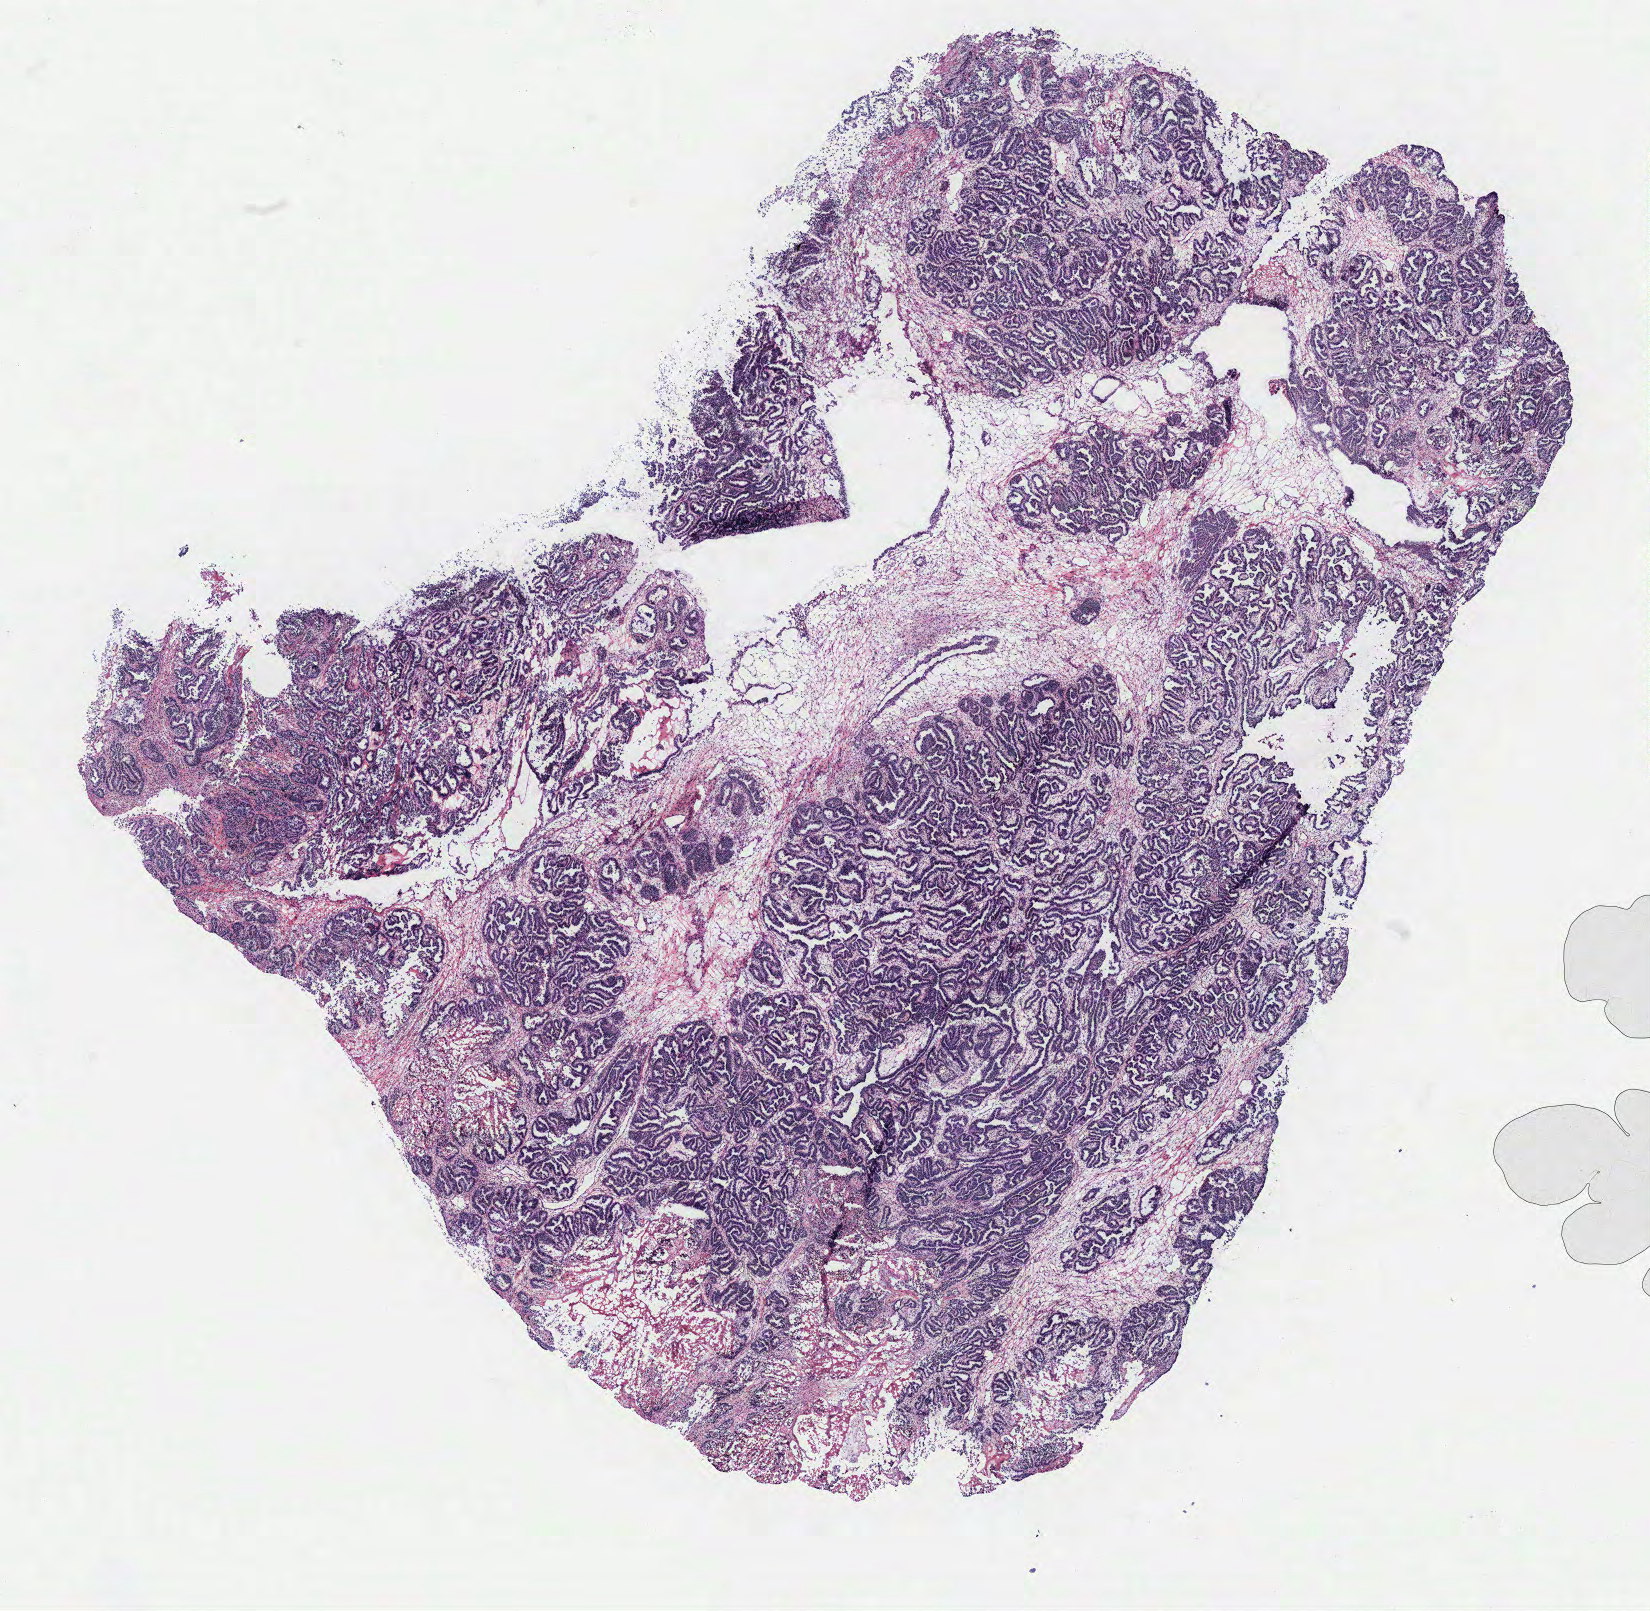
Whole-slide histology image, H&E-stained, whole scanned area (about 13.2 x 12.9 mm, acquisition: 40x scan) shown as a low-resolution overview; ovary, tumour tissue. Patient: female, age 55 years.
Primary tumour site (as recorded): fallopian tube. Diagnosis: Serous adenocarcinoma, NOS (fallopian tube).